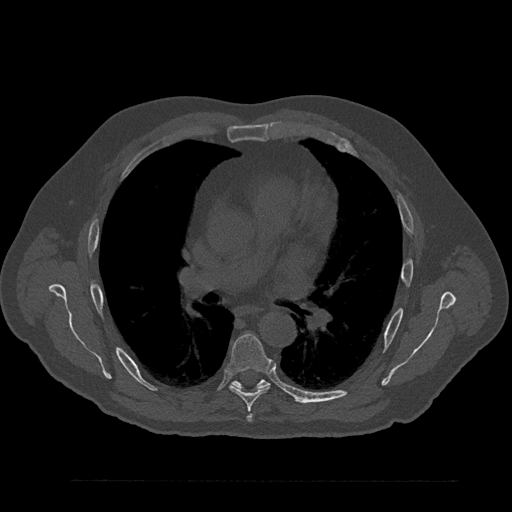
CT including the spine, one axial slice. Slice 541 of 797 in the series (ordered by position). Reconstruction kernel Br40s/3. 120 kVp. Bone window (W 1800 / L 400 HU). 0.5 mm slice thickness. 512 × 512 image matrix, field of view 430 × 430 mm. Patient: male, 61 years. Case-level facts recorded for this patient, not image findings: primary cancer: prostate.
Annotated regions visible in this slice (semi-automatically segmented with operator editing):
- T6 vertebra: bounding box <226,334,272,422> (left, top, right, bottom; pixels)
- T7 vertebra: <233,380,269,389>